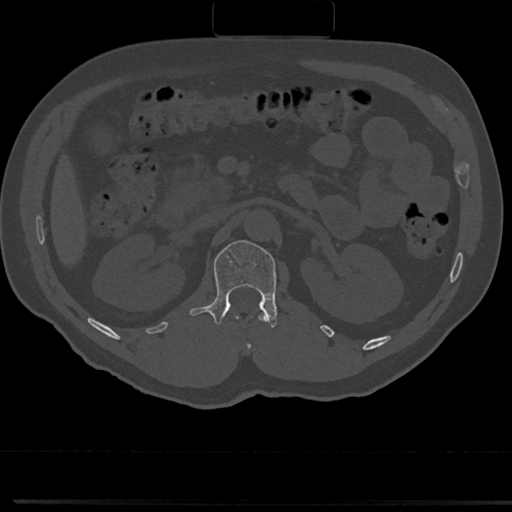
CT including the spine, one axial slice. Slice 96 of 817 in the series (ordered by position). Reconstruction kernel Br40s/3. 120 kVp. Bone window (W 1800 / L 400 HU). 0.5 mm slice thickness. 512 × 512 image matrix, field of view 355 × 355 mm. Male patient, age 61 years. Case-level facts recorded for this patient, not image findings: primary cancer: prostate.
Outlined on this slice (semi-automatically segmented with operator editing):
- L1 vertebra: box from (x=191, y=240) to (x=278, y=327) px
- T12 vertebra: (x=248, y=314)–(x=266, y=347)